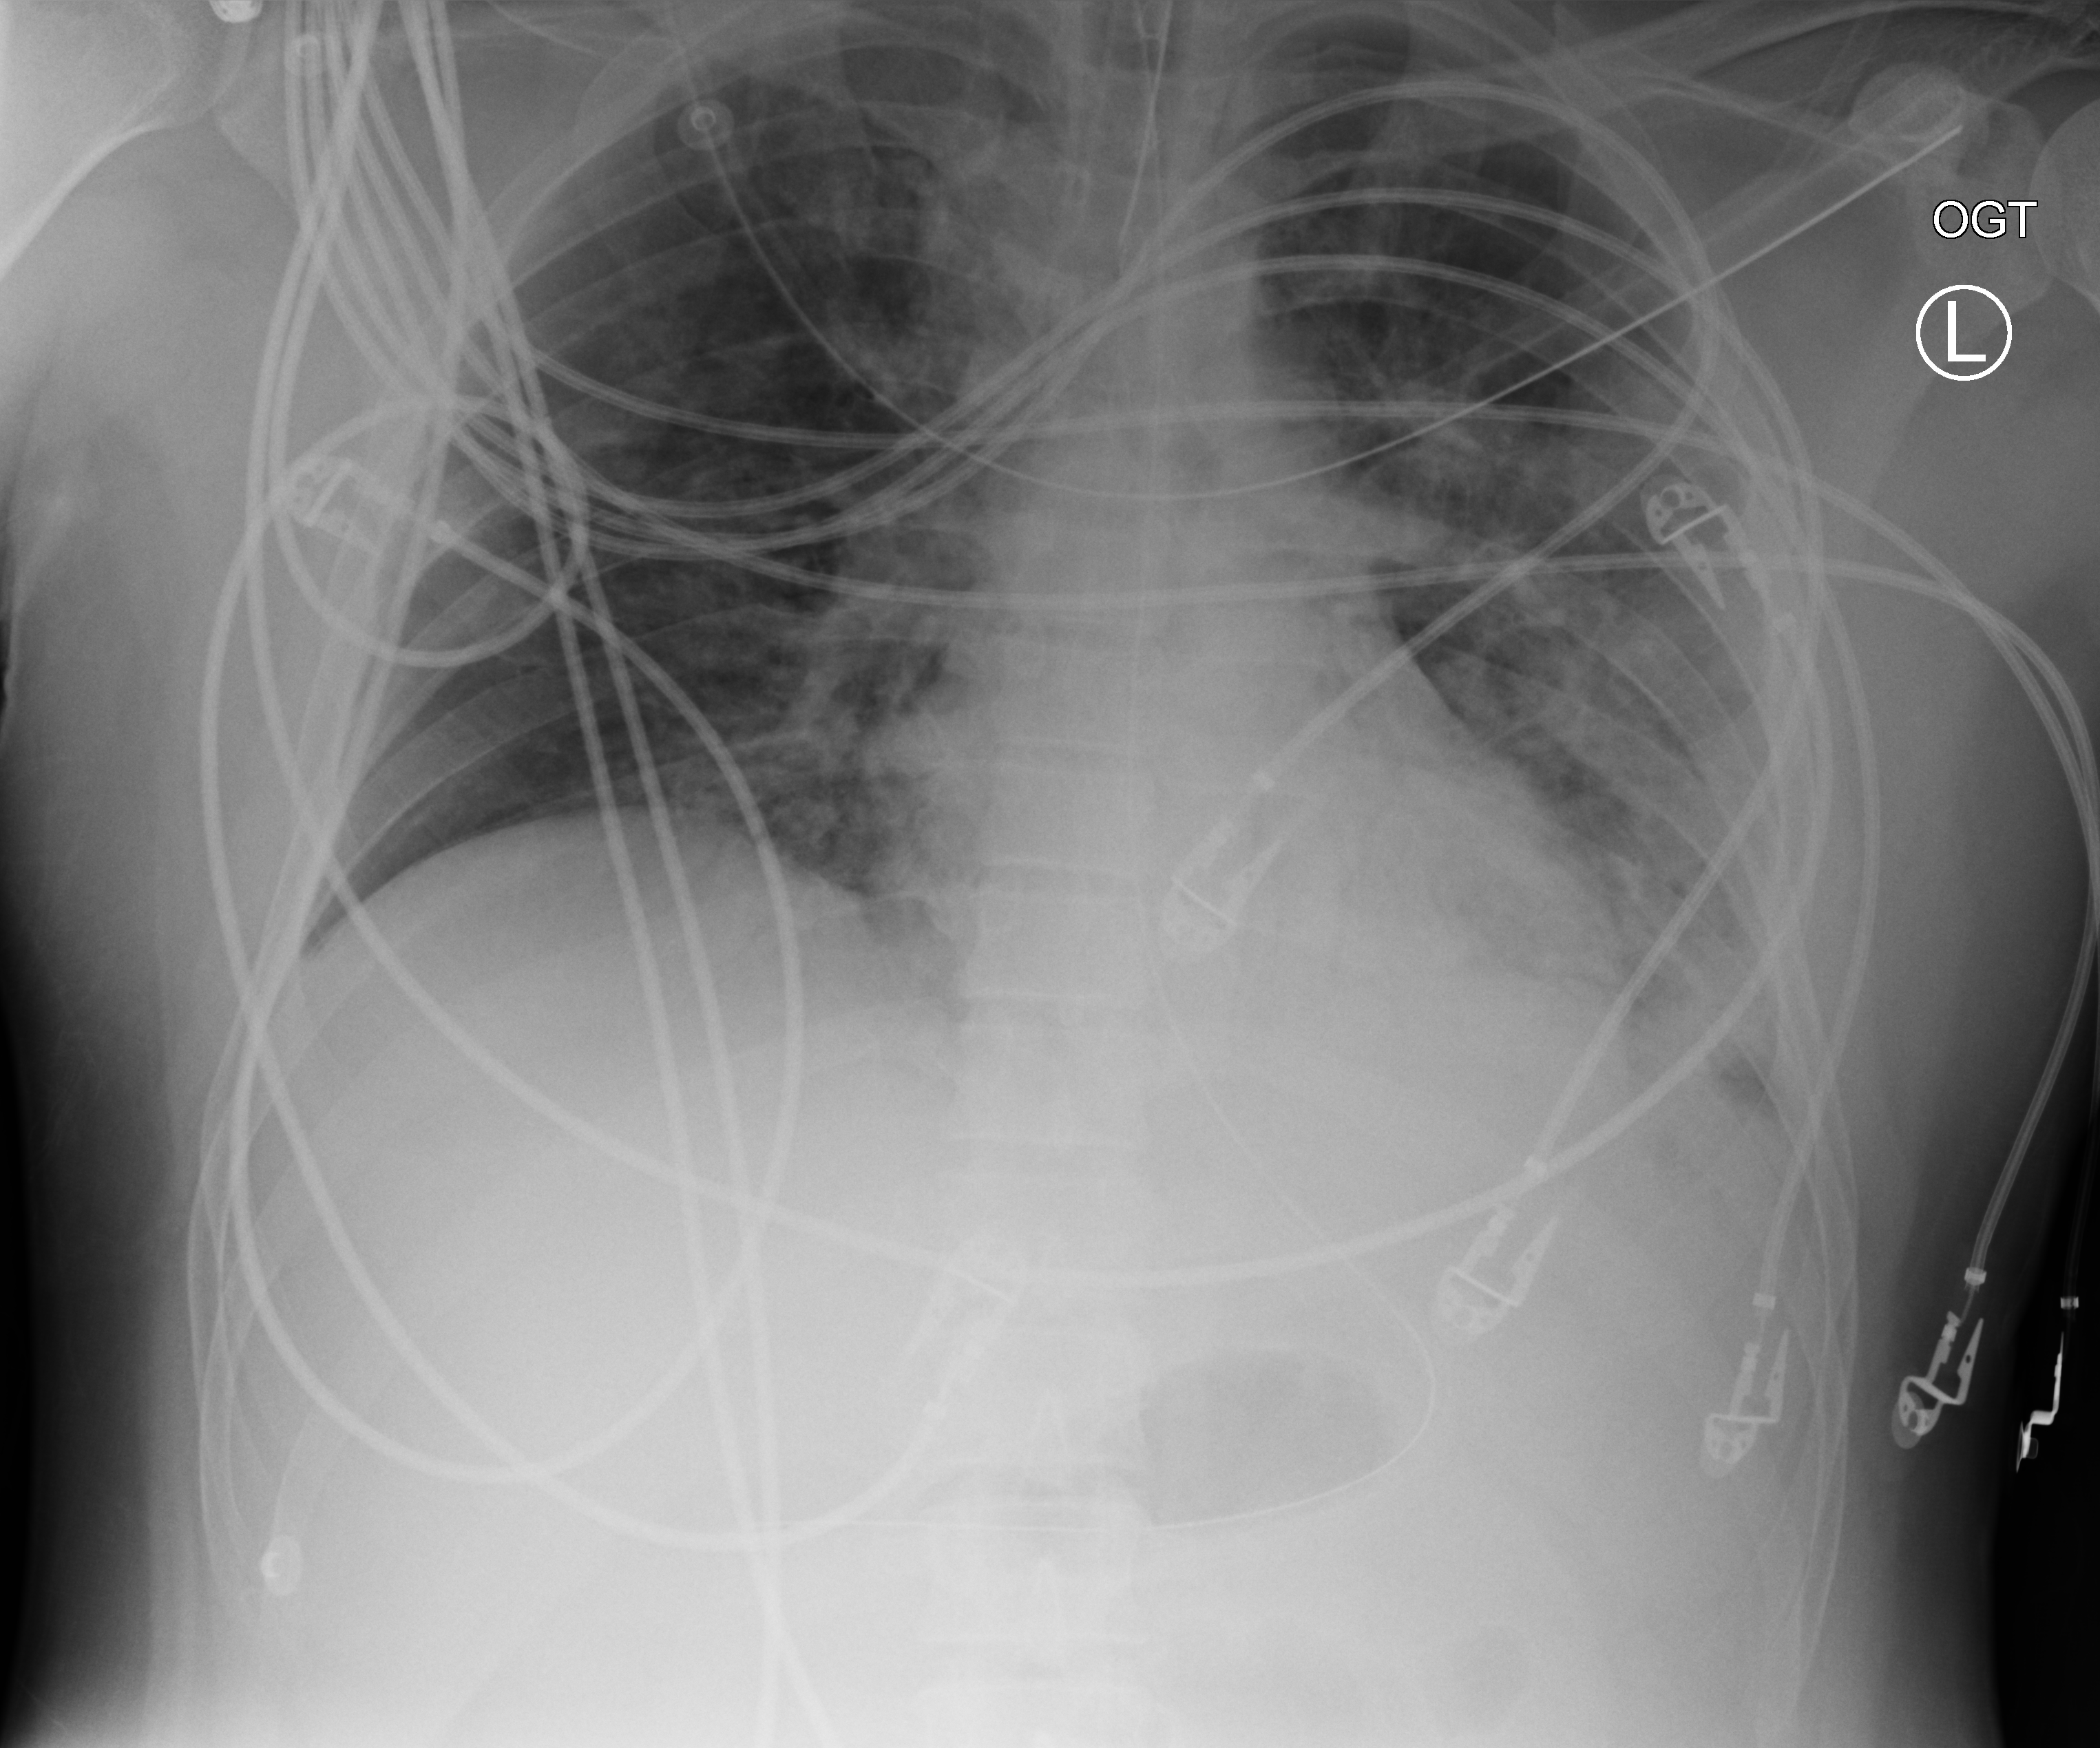
Bedside chest radiograph (computed radiography). Adult patient hospitalised with COVID-19, age 18–59 years.
Admission-level facts for this patient (not findings on this image; timing relative to this image not recorded):
- mechanically ventilated during this hospital stay: yes
- admitted to intensive care during this hospital stay: yes